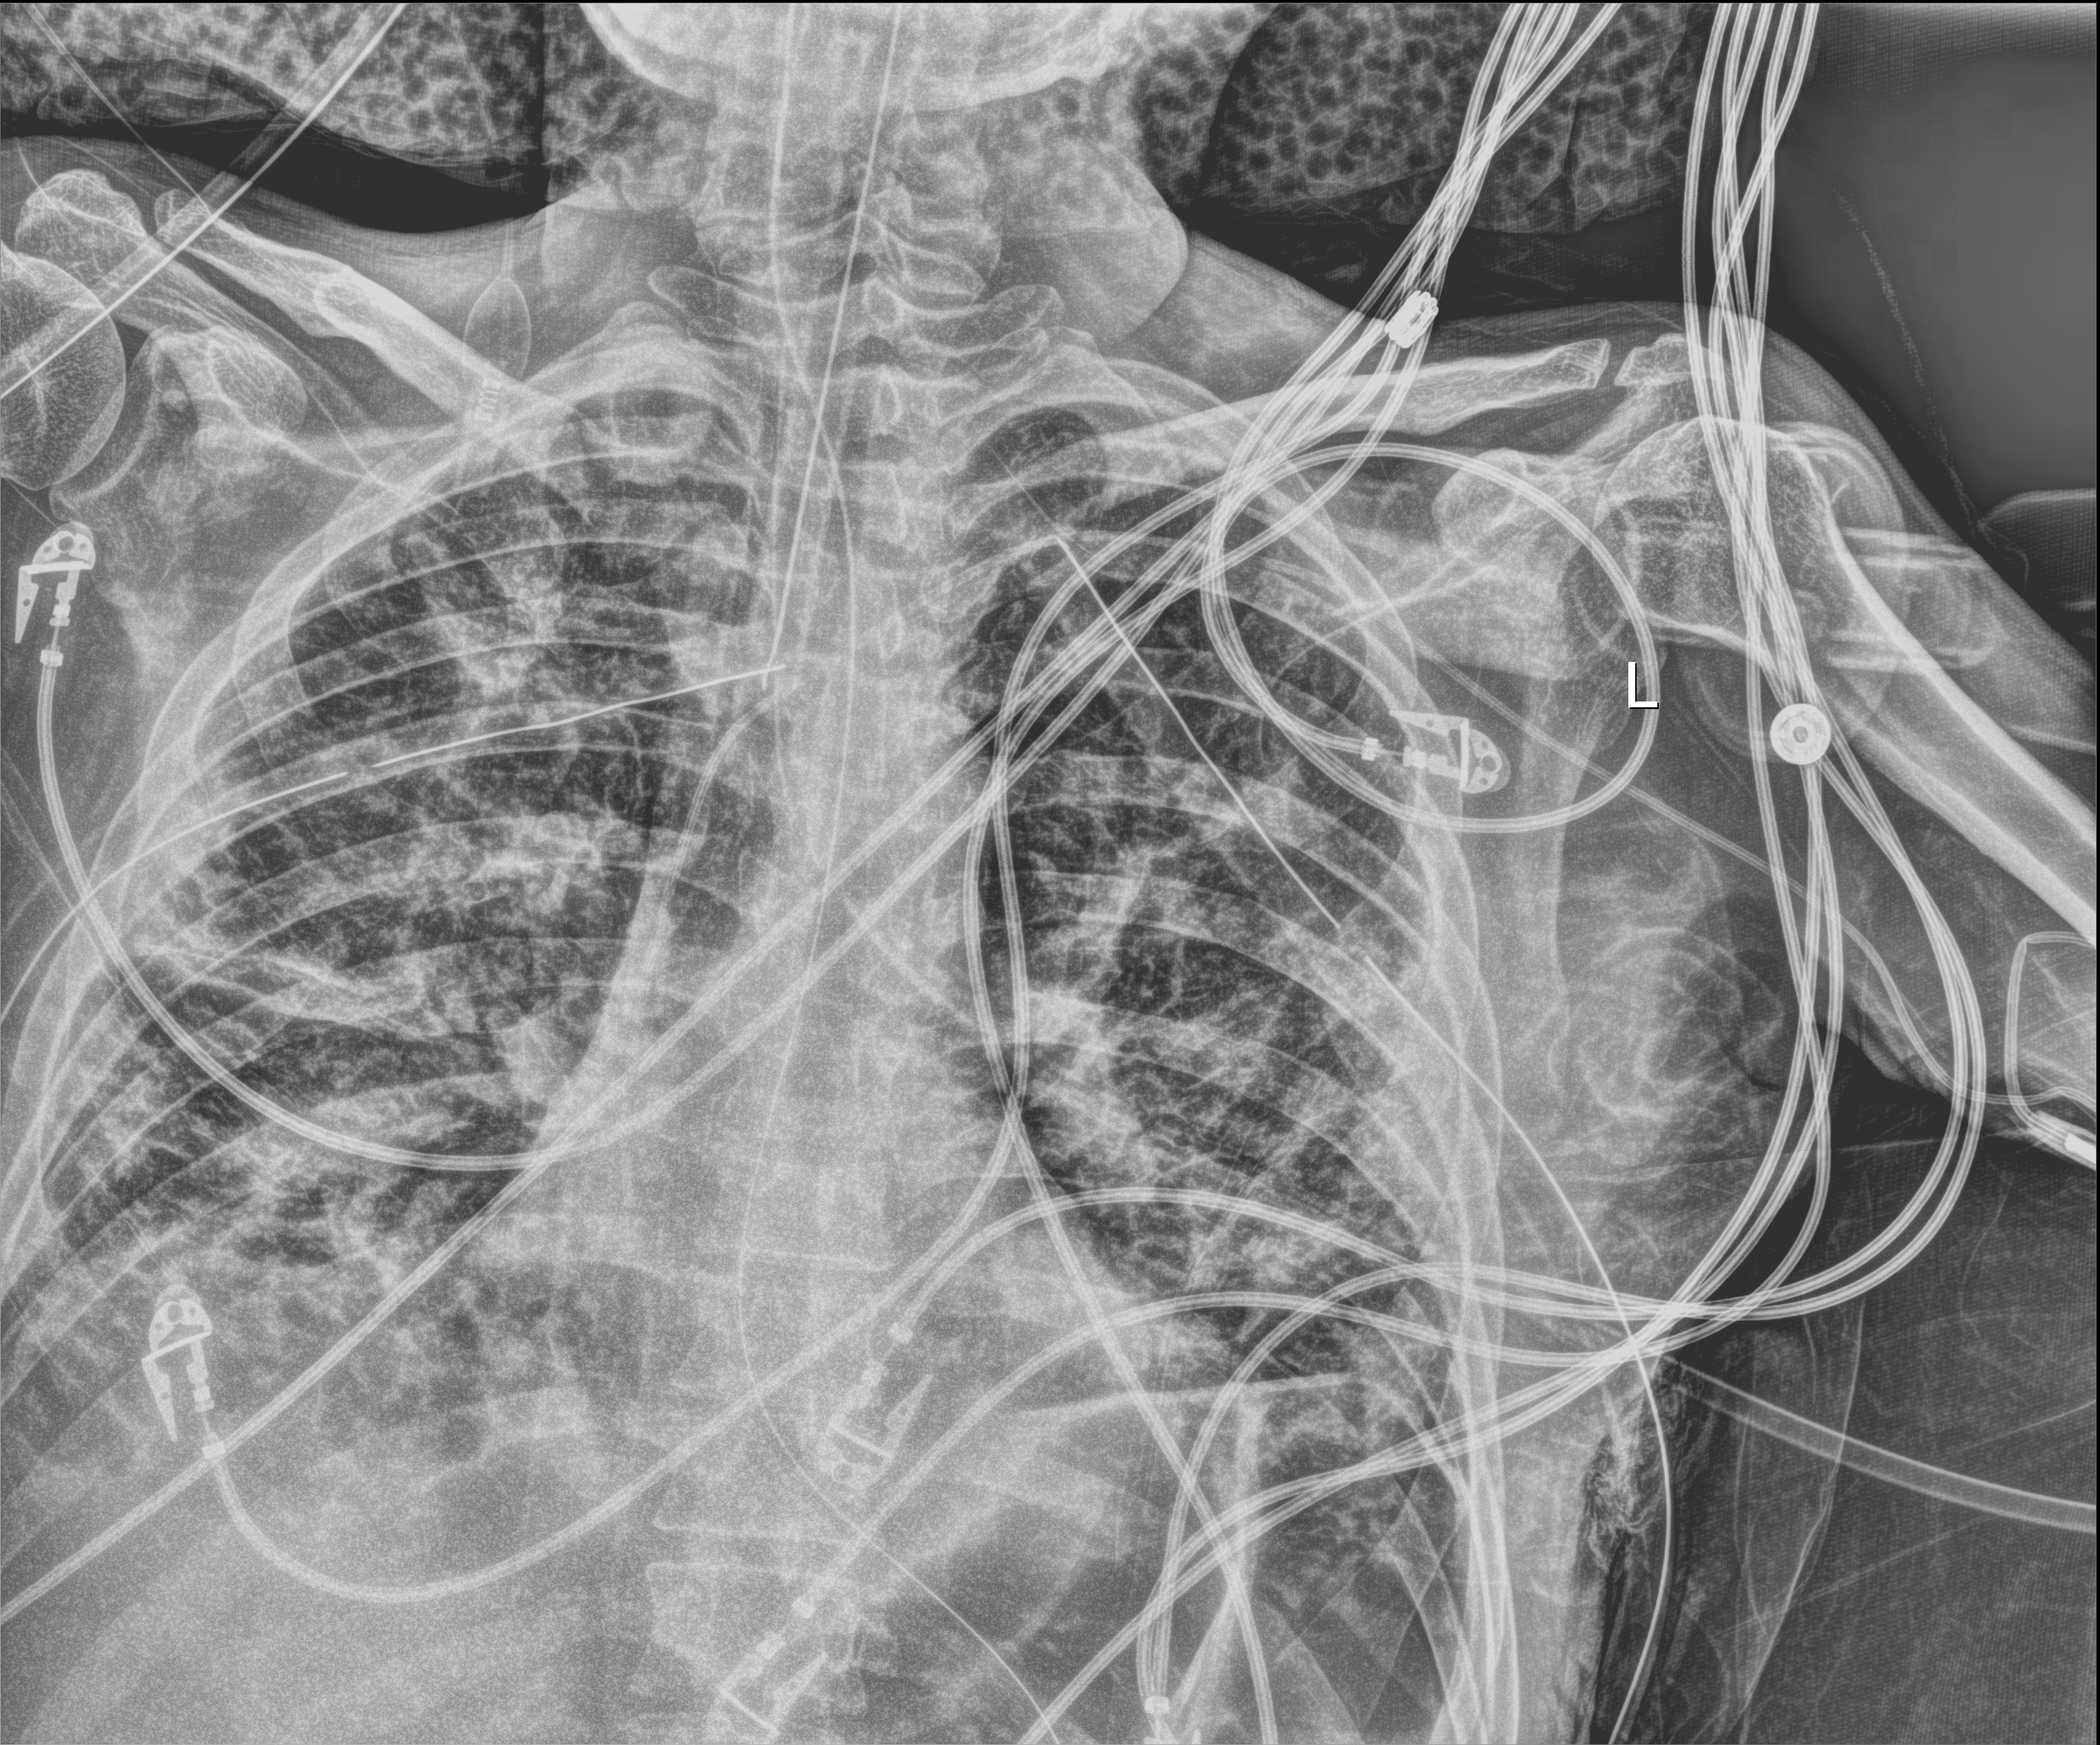
Portable chest radiograph, anteroposterior (AP) projection. Male patient hospitalised with COVID-19, age 18–59 years.
Hospital-stay facts (about this admission, not read from this image; timing relative to this image not recorded): admitted to intensive care during this hospital stay: yes; length of hospital stay: 96 days.